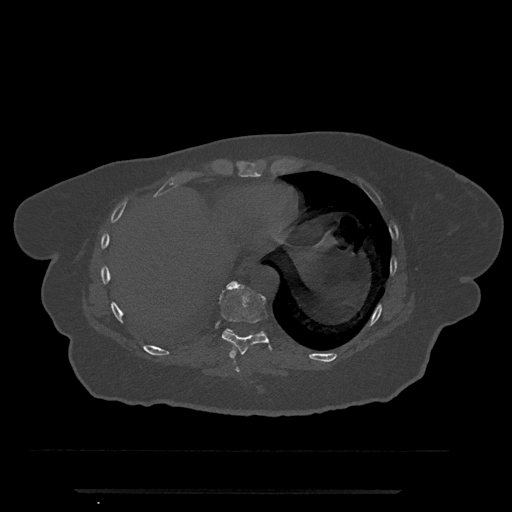
CT including the spine, one axial slice; position 330 of 797 along the scan axis; bone window (W 1800 / L 400 HU); 512 × 512 image matrix, field of view 440 × 440 mm. Patient: female, 51 years. From the clinical record (not read from this slice): primary cancer: neuro; vertebrae with lytic lesions (as recorded): T8.
Structures marked on this image (semi-automatic segmentation, software-assisted and operator-edited):
- T10 vertebra: bounding box <226,329,263,334> (left, top, right, bottom; pixels)
- T8 vertebra: <235,367,240,373>
- T9 vertebra: <210,281,273,358>